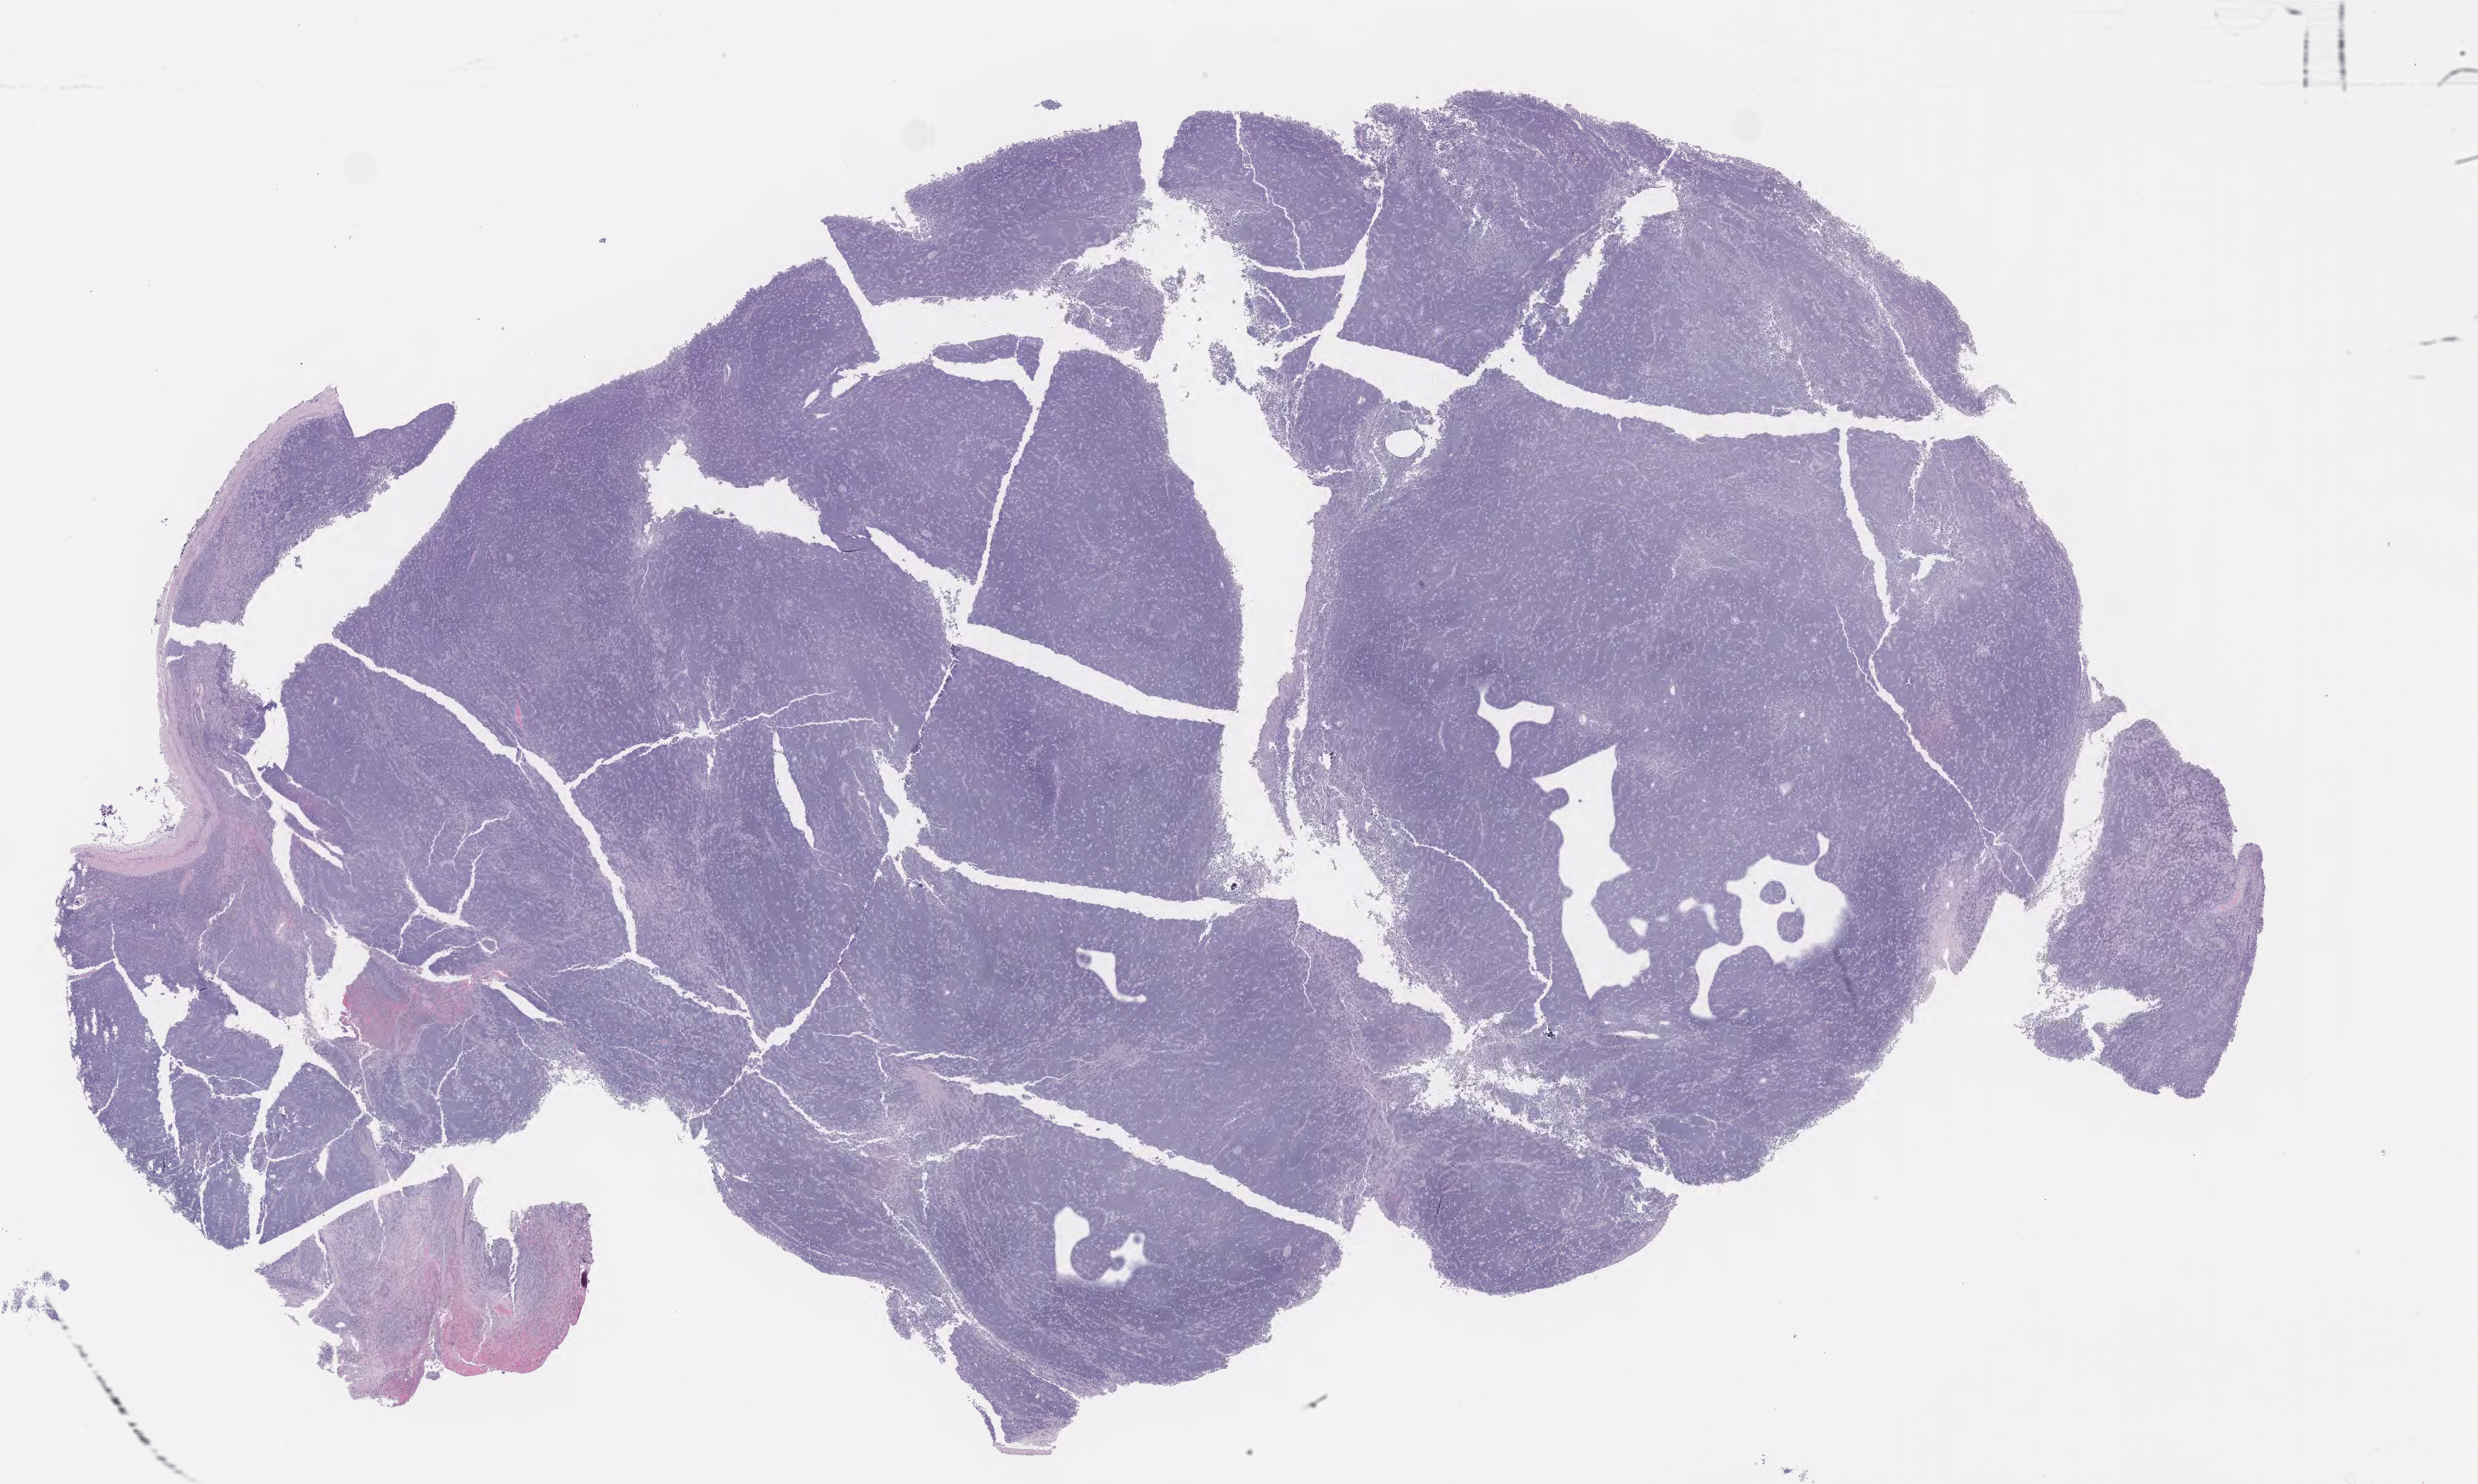
H&E whole-slide image — a low-resolution overview of the entire scanned area, about 28.2 x 16.9 mm, tumor tissue, anatomic site: head and neck. Patient: male, 30 years old.
• diagnosis: Burkitt lymphoma, NOS